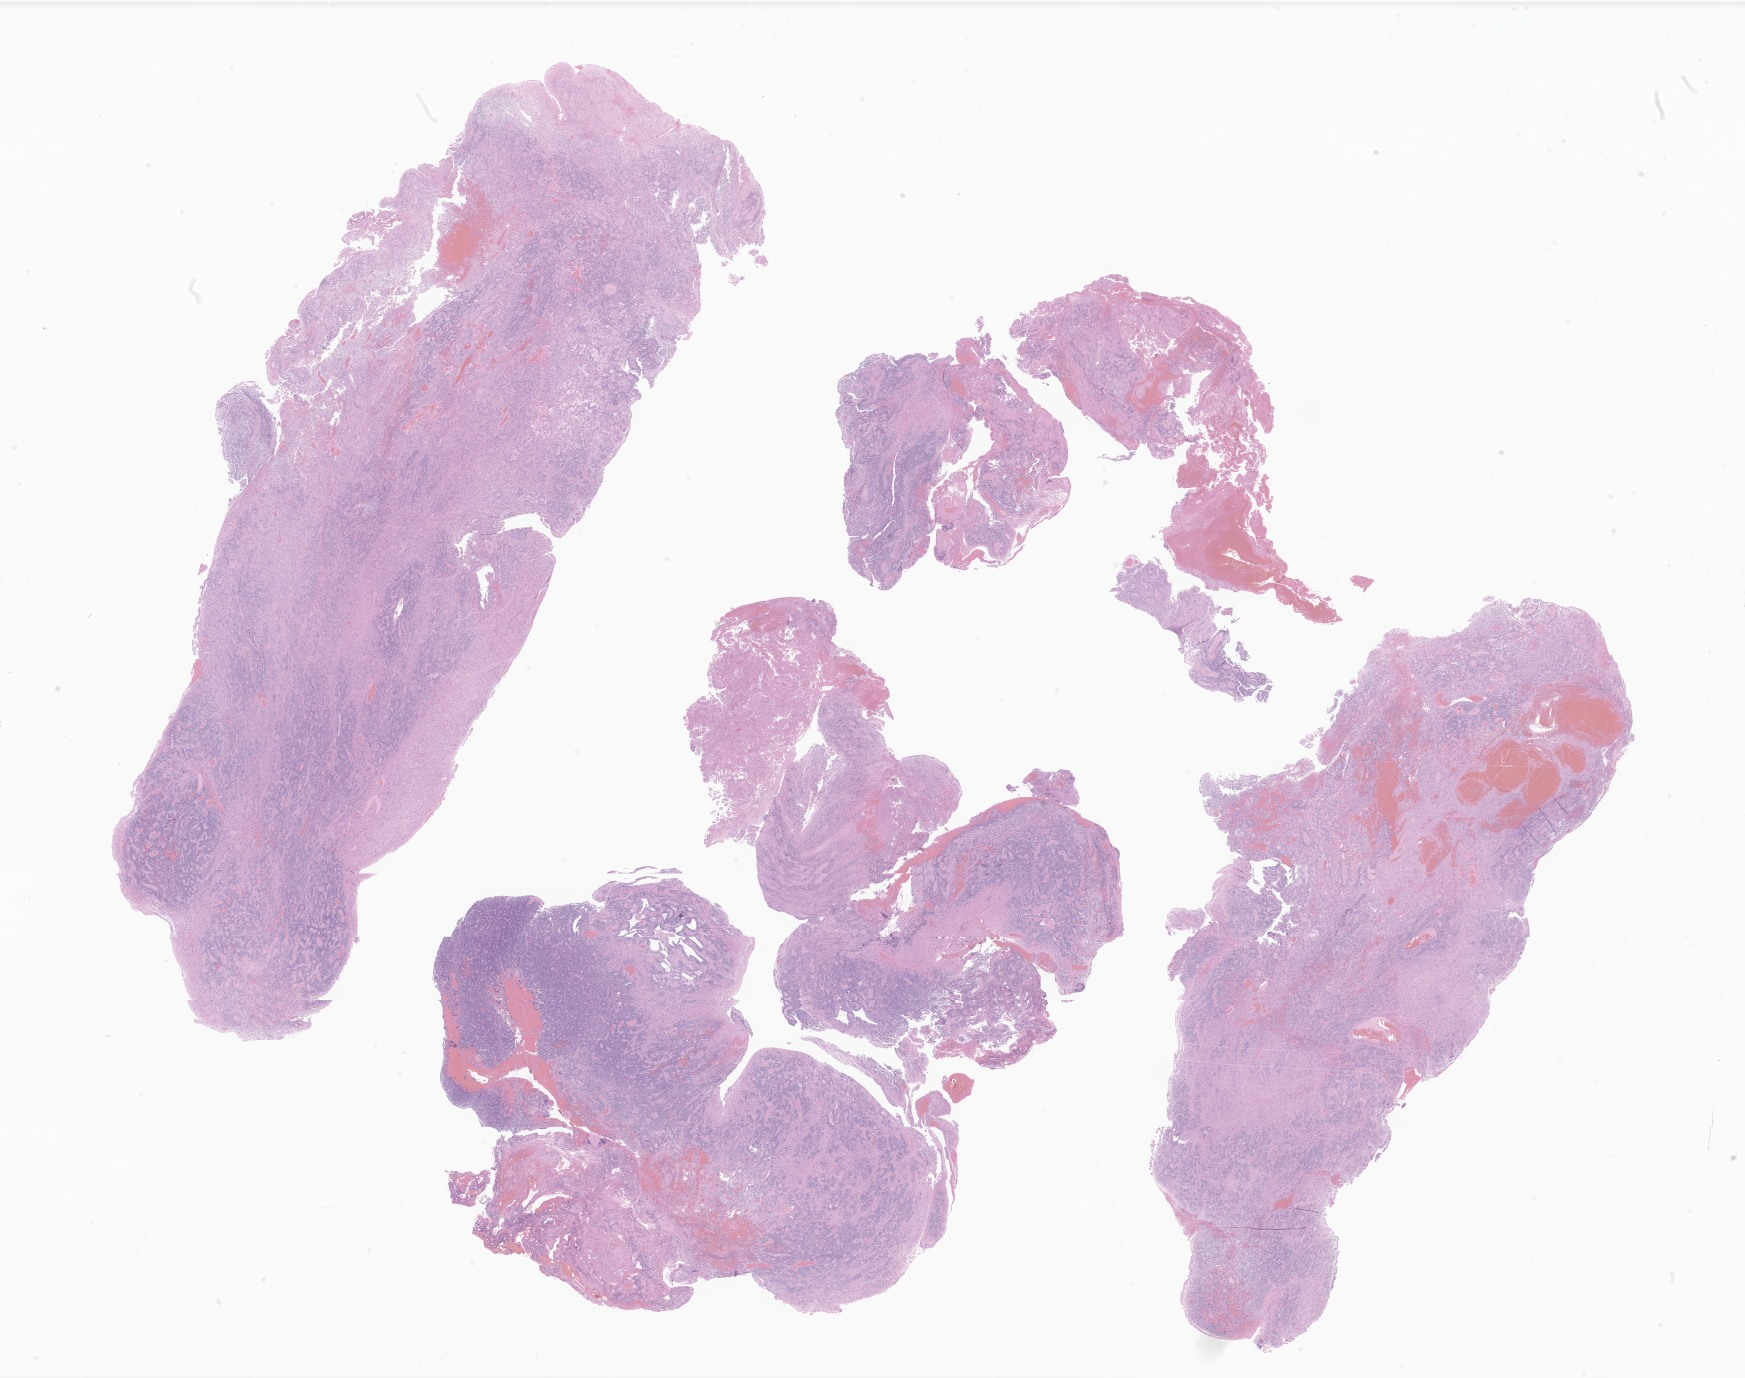
Haematoxylin and eosin whole-slide image of tumor tissue from the cerebellum, low-resolution overview of the scanned area, about 29.4 x 23.2 mm. FFPE section. Patient: female, age 153 months (12 years 9 months).
• recorded diagnosis: Ependymoma, NOS